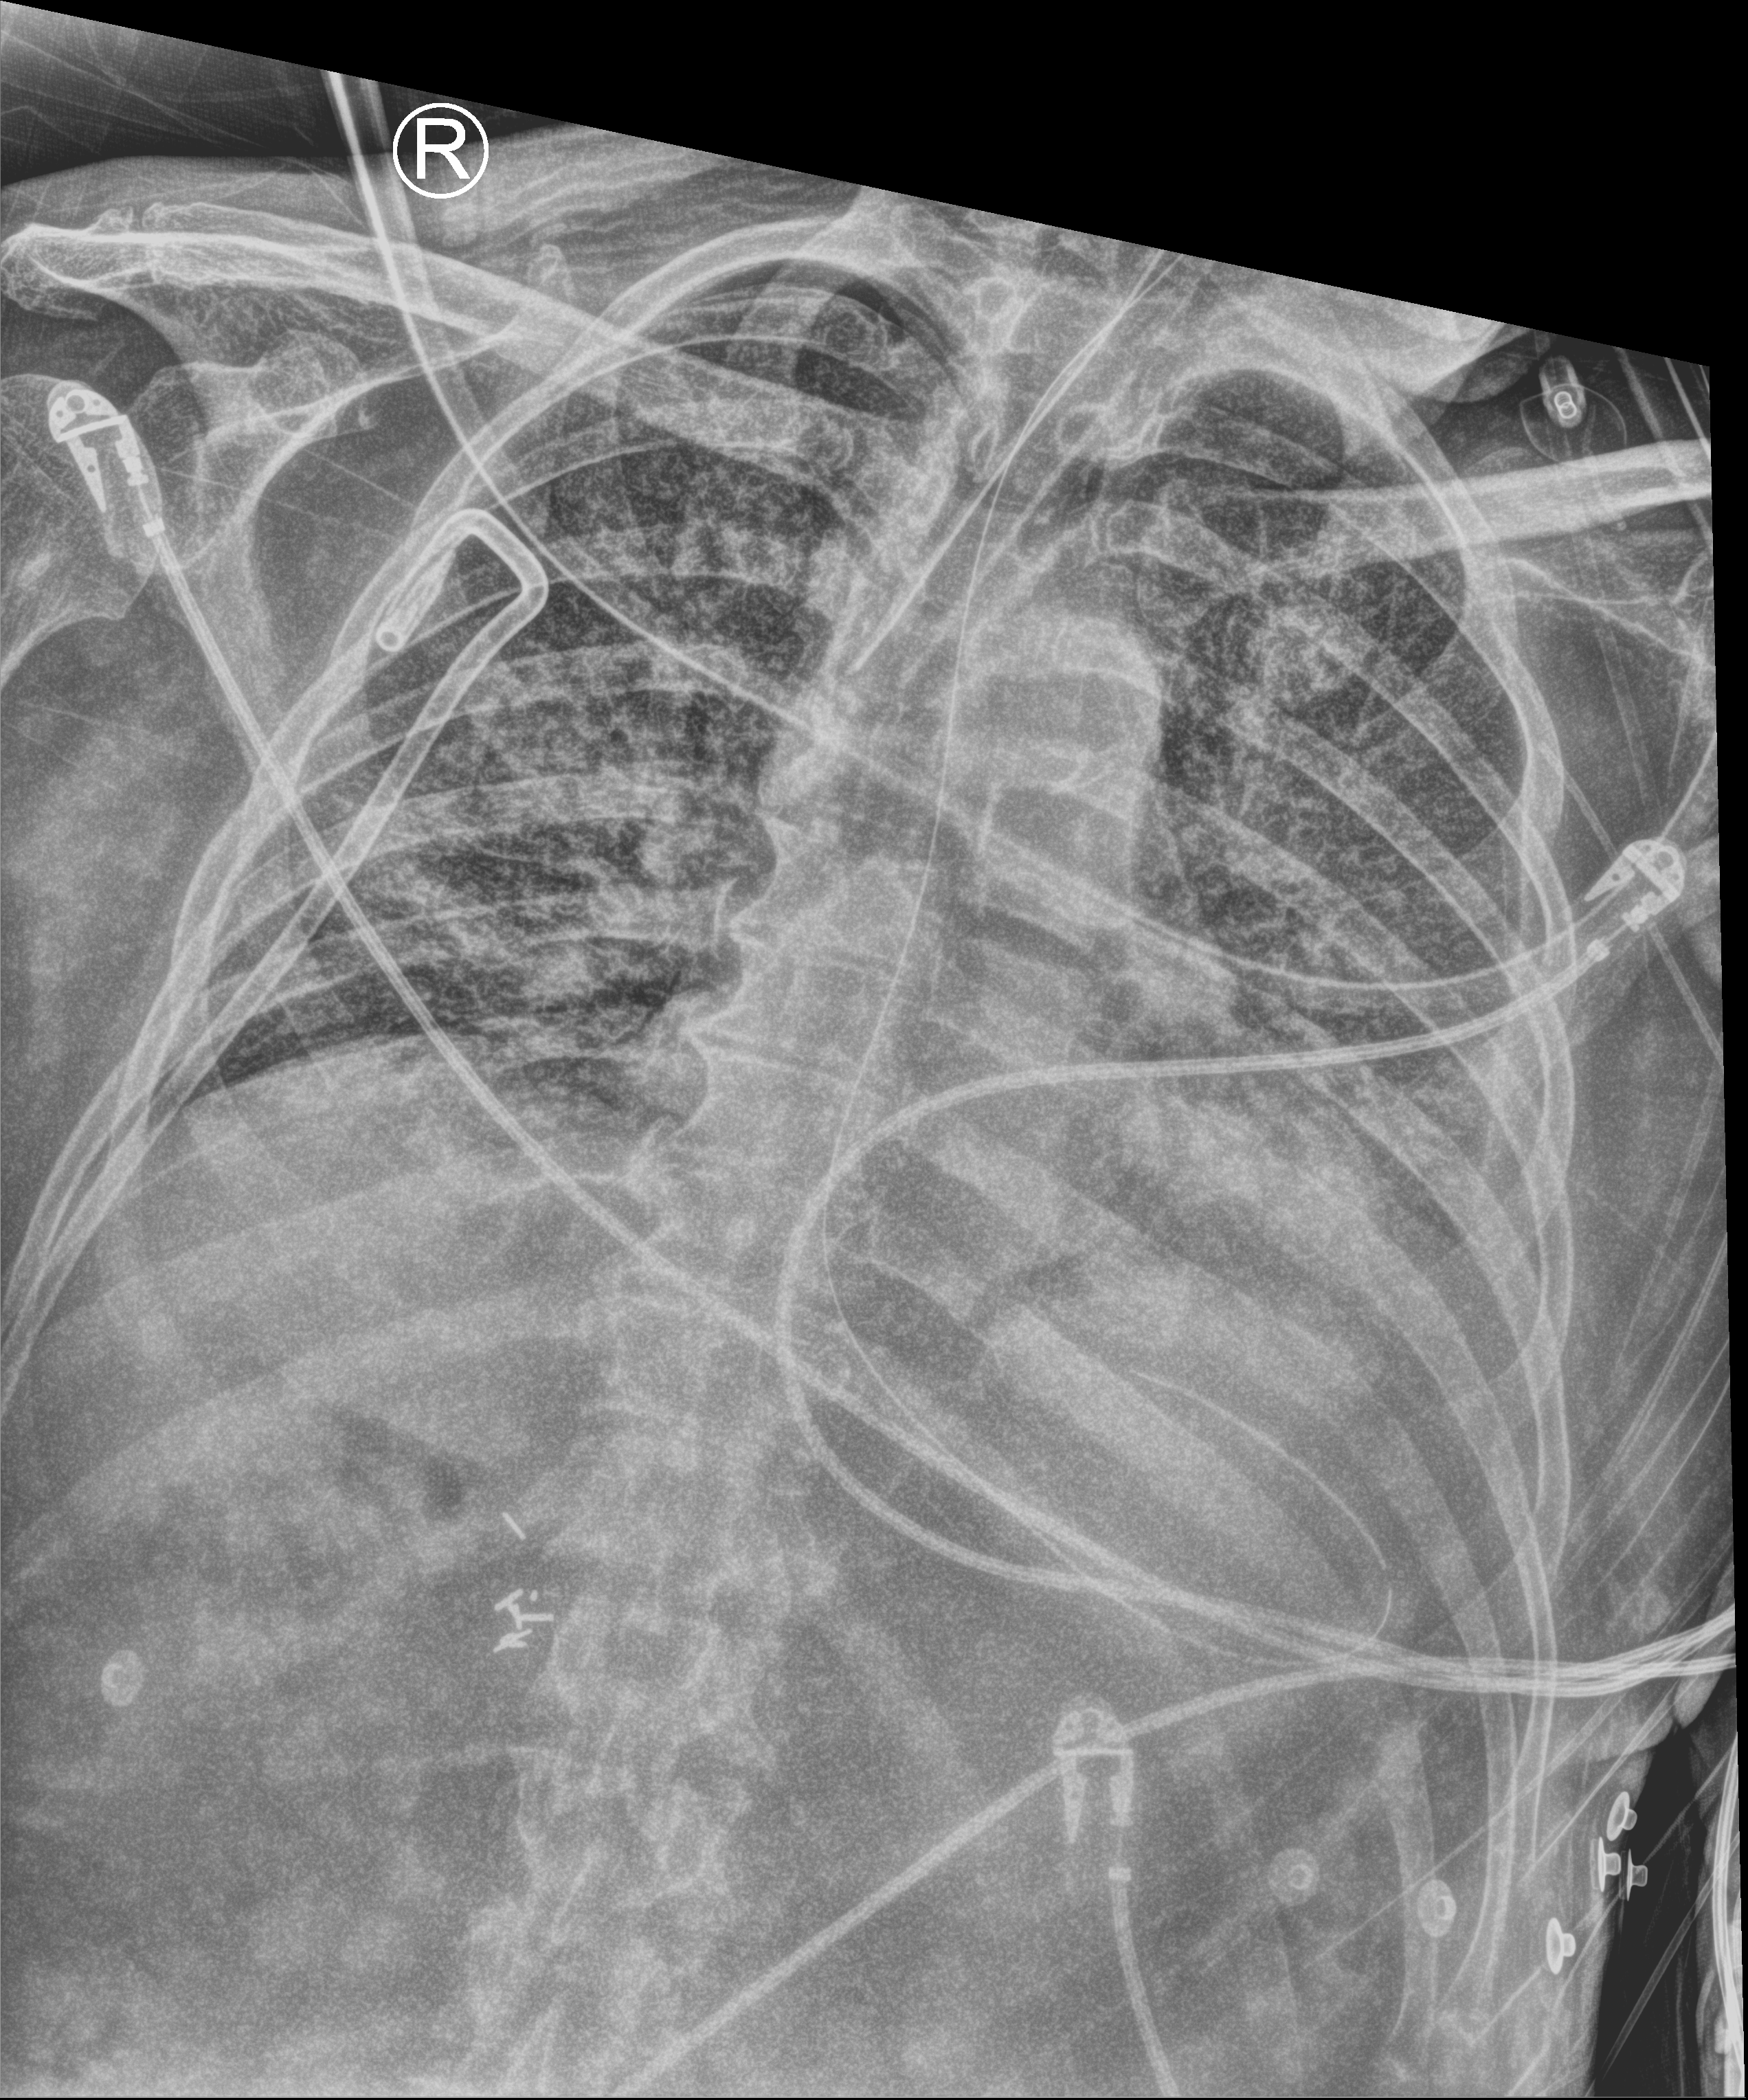
Chest X-ray (portable). Patient hospitalised with COVID-19; male, aged 75–90 years.
Admission-level facts for this patient (not findings on this image; timing relative to this image not recorded): diabetes (admission record): no.